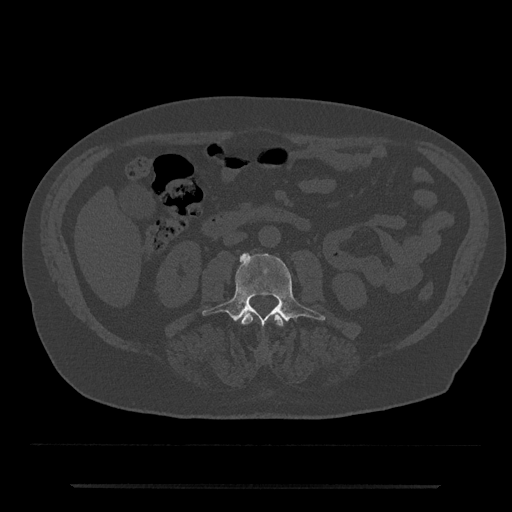
CT including the spine, one axial slice; position 421 of 797 along the scan axis; reconstruction kernel Br40s/3; 120 kVp; bone window (W 1800 / L 400 HU); 512 × 512 image matrix, field of view 434 × 434 mm. Male patient, age 80 years. From the clinical record (not read from this slice): primary cancer: prostate; vertebrae with lytic lesions (as recorded): L1, T11.
Outlined on this slice (semi-automatically segmented with operator editing):
- L2 vertebra: bounding box (x1, y1, x2, y2) in pixels: (242, 312, 284, 326)
- L3 vertebra: (202, 252, 326, 327)